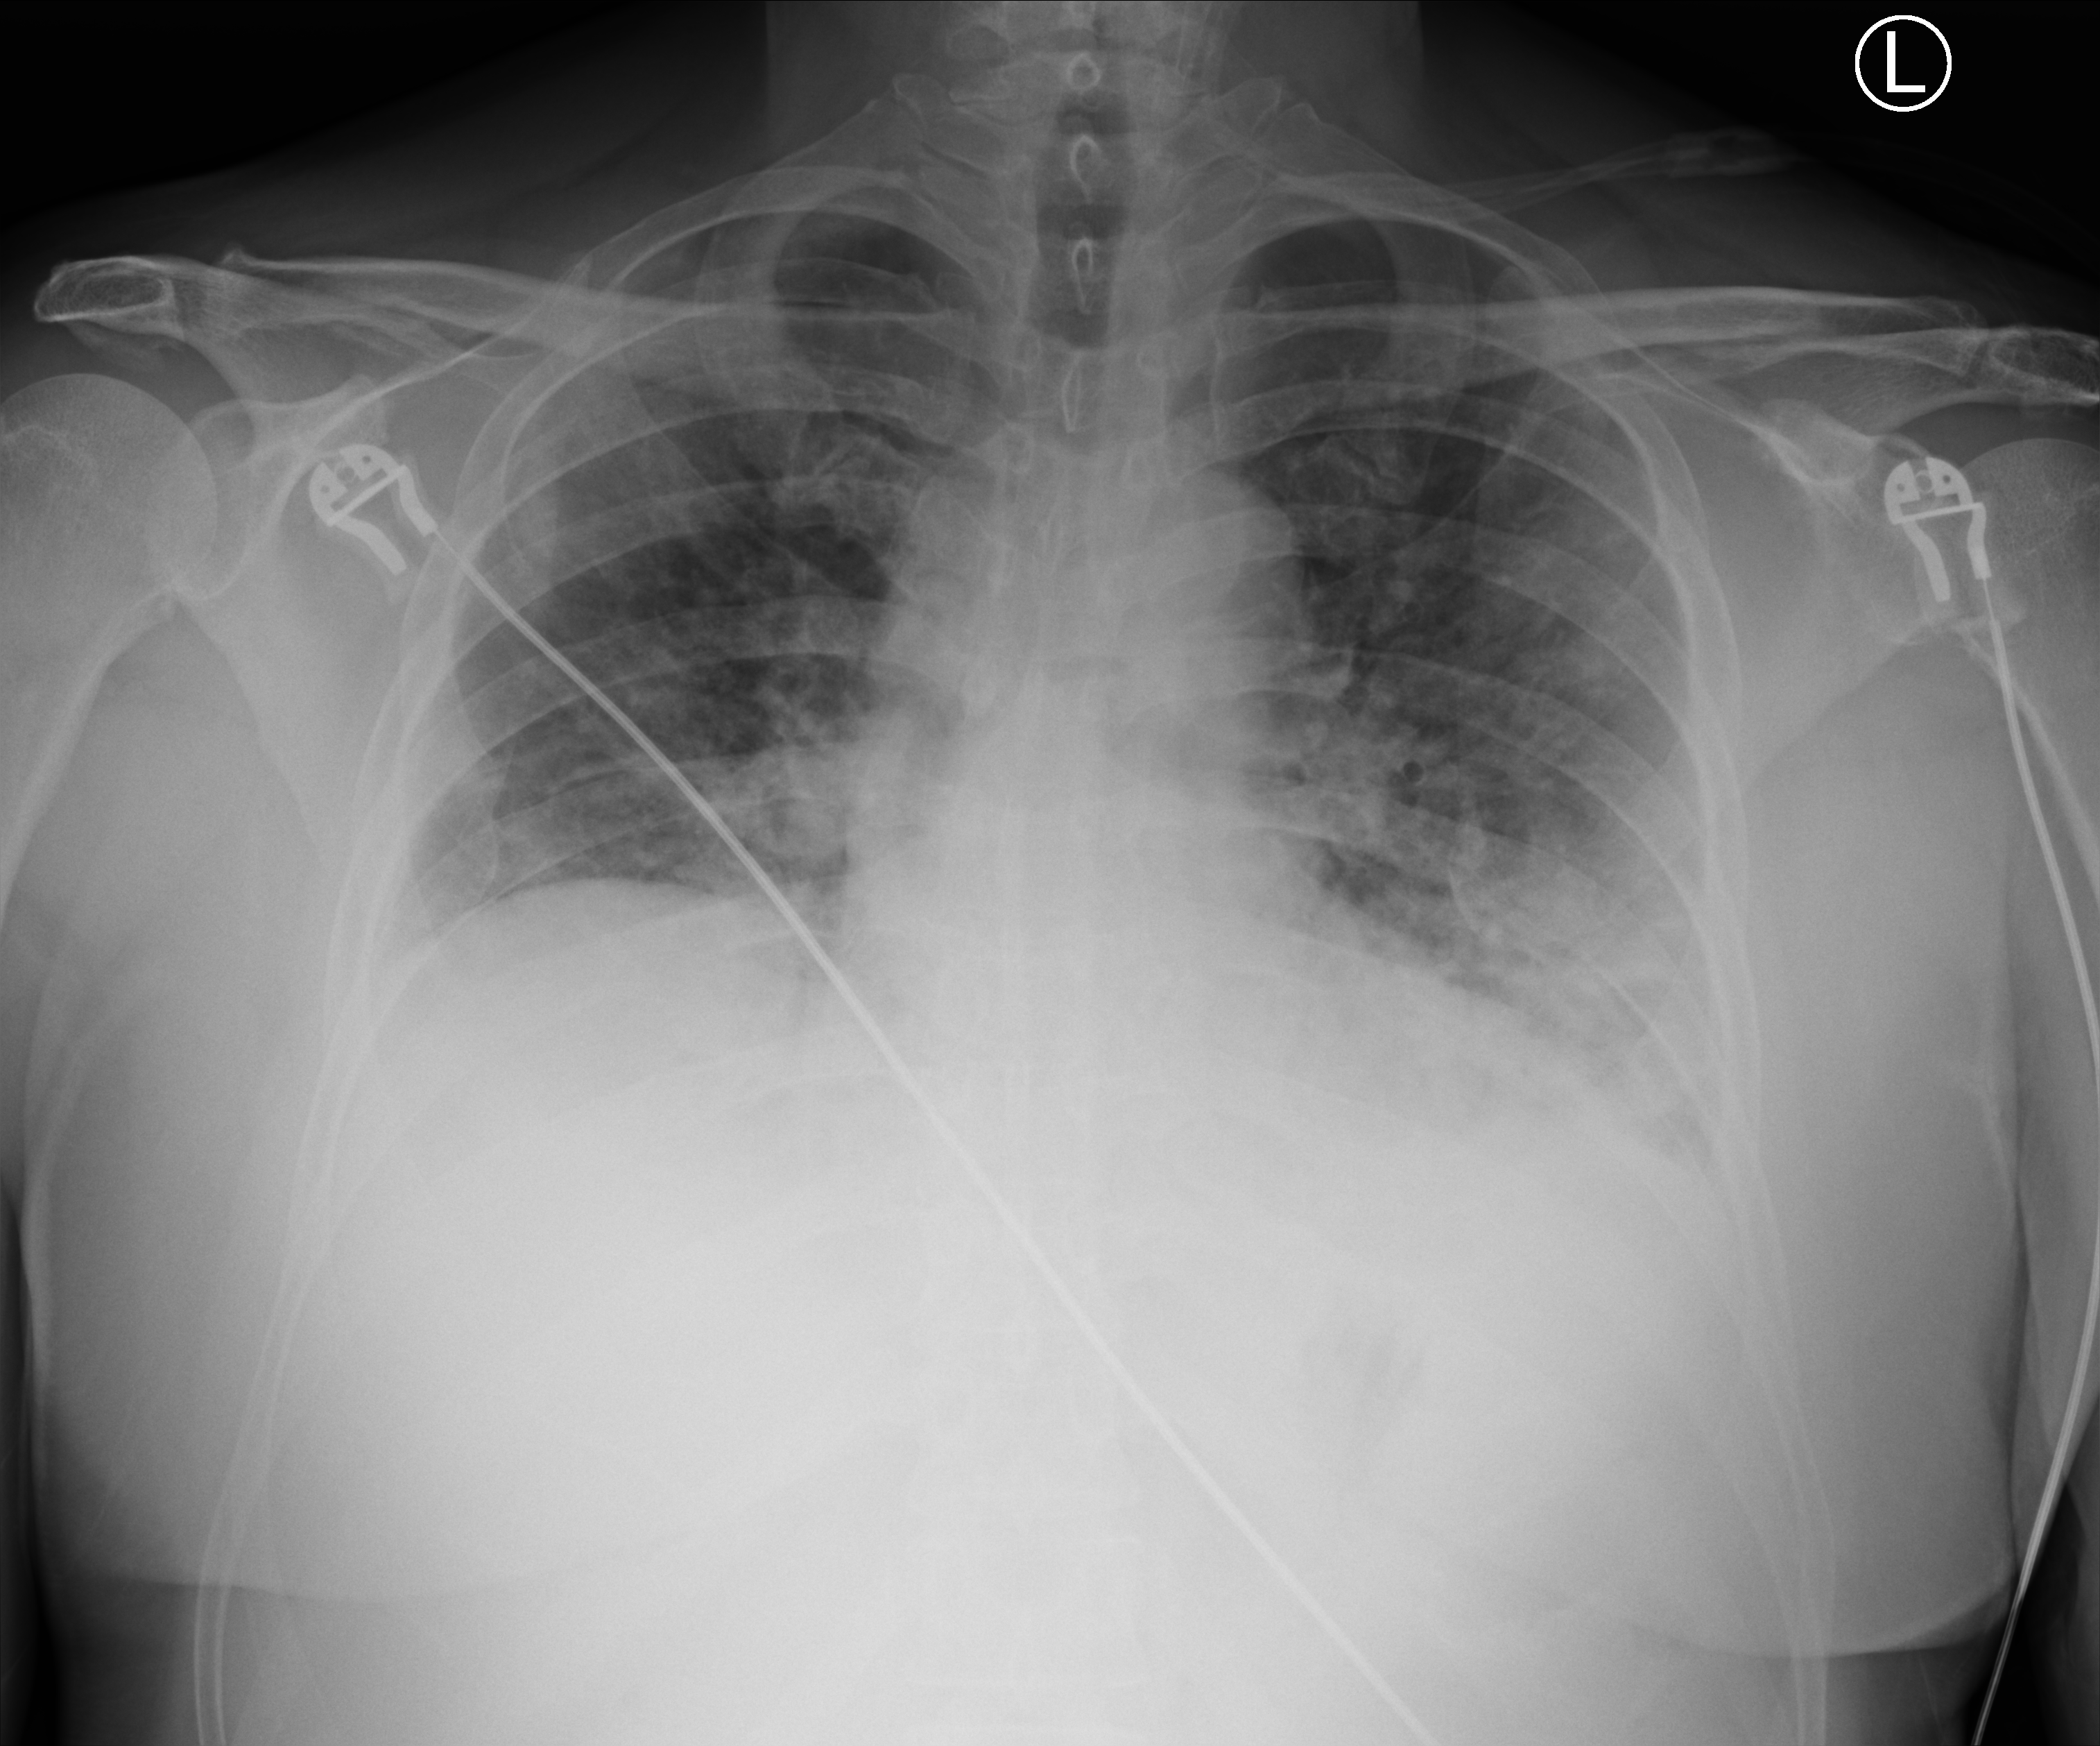
Bedside chest radiograph (computed radiography), anteroposterior (AP) projection. Patient hospitalised with COVID-19; male, aged 18–59 years.
Admission-level facts for this patient (not findings on this image; timing relative to this image not recorded):
- hypertension (admission record): no